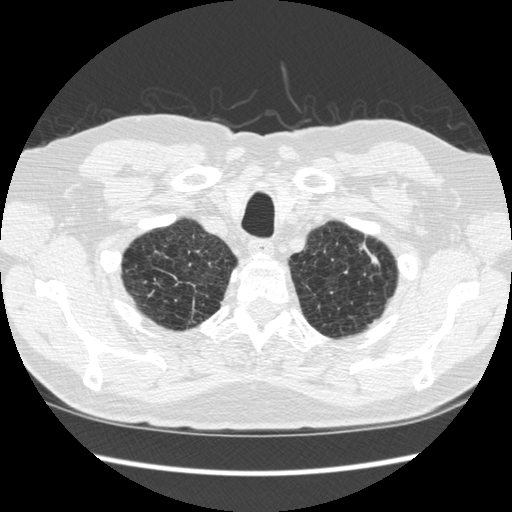
Axial slice from a low-dose chest CT screening exam. Second annual screen. Lung window (W 1500 / L -600 HU). 1.25 mm slice thickness. Standard (soft-tissue) reconstruction kernel (STANDARD). 512 × 512 image matrix. Male, age 70 years at enrolment. Former smoker at enrolment.
- Expert reader's lesion annotation, bounding box [x1, y1, x2, y2] px = [325, 232, 387, 301].
- The screening reader recorded 5 non-calcified nodules or masses ≥4 mm on this exam (right lower lobe, right lower lobe, right lower lobe, left upper lobe, left lower lobe); which of them this box marks is not recorded.
- Official screen result: positive, change unspecified: nodule(s) >= 4 mm or enlarging nodule(s), mass(es), or other non-specific abnormalities suspicious for lung cancer.
- Participant outcome: lung cancer diagnosed 479 days after this screen — squamous cell carcinoma, NOS, left upper lobe, moderately differentiated (G2), stage IA (AJCC 6th edition), 18 mm at pathology.